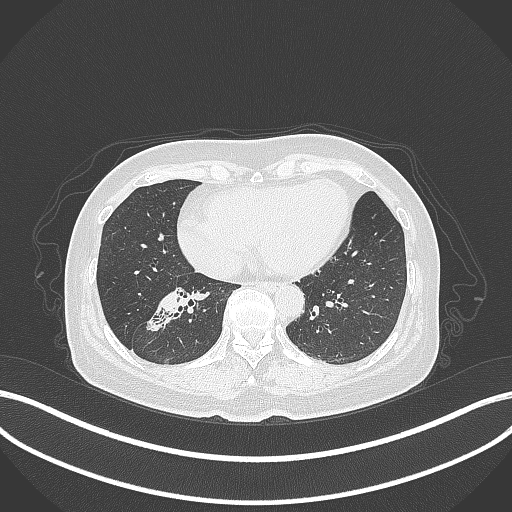
Chest CT, one axial slice; position 138 of 429 along the scan axis; 120 kVp; lung window (W 1500 / L -600 HU); 512 × 512 image matrix, field of view 400 × 400 mm. Patient: female, 67 years. From the clinical record (not read from this slice): clinical TNM (as recorded): T1c N1 M0; histopathological grade: G2-3.
Outlined on this slice (bounding box drawn by a radiologist):
- lung tumour (recorded histology: adenocarcinoma): bounding box [x1, y1, x2, y2] px = [144, 287, 194, 330]